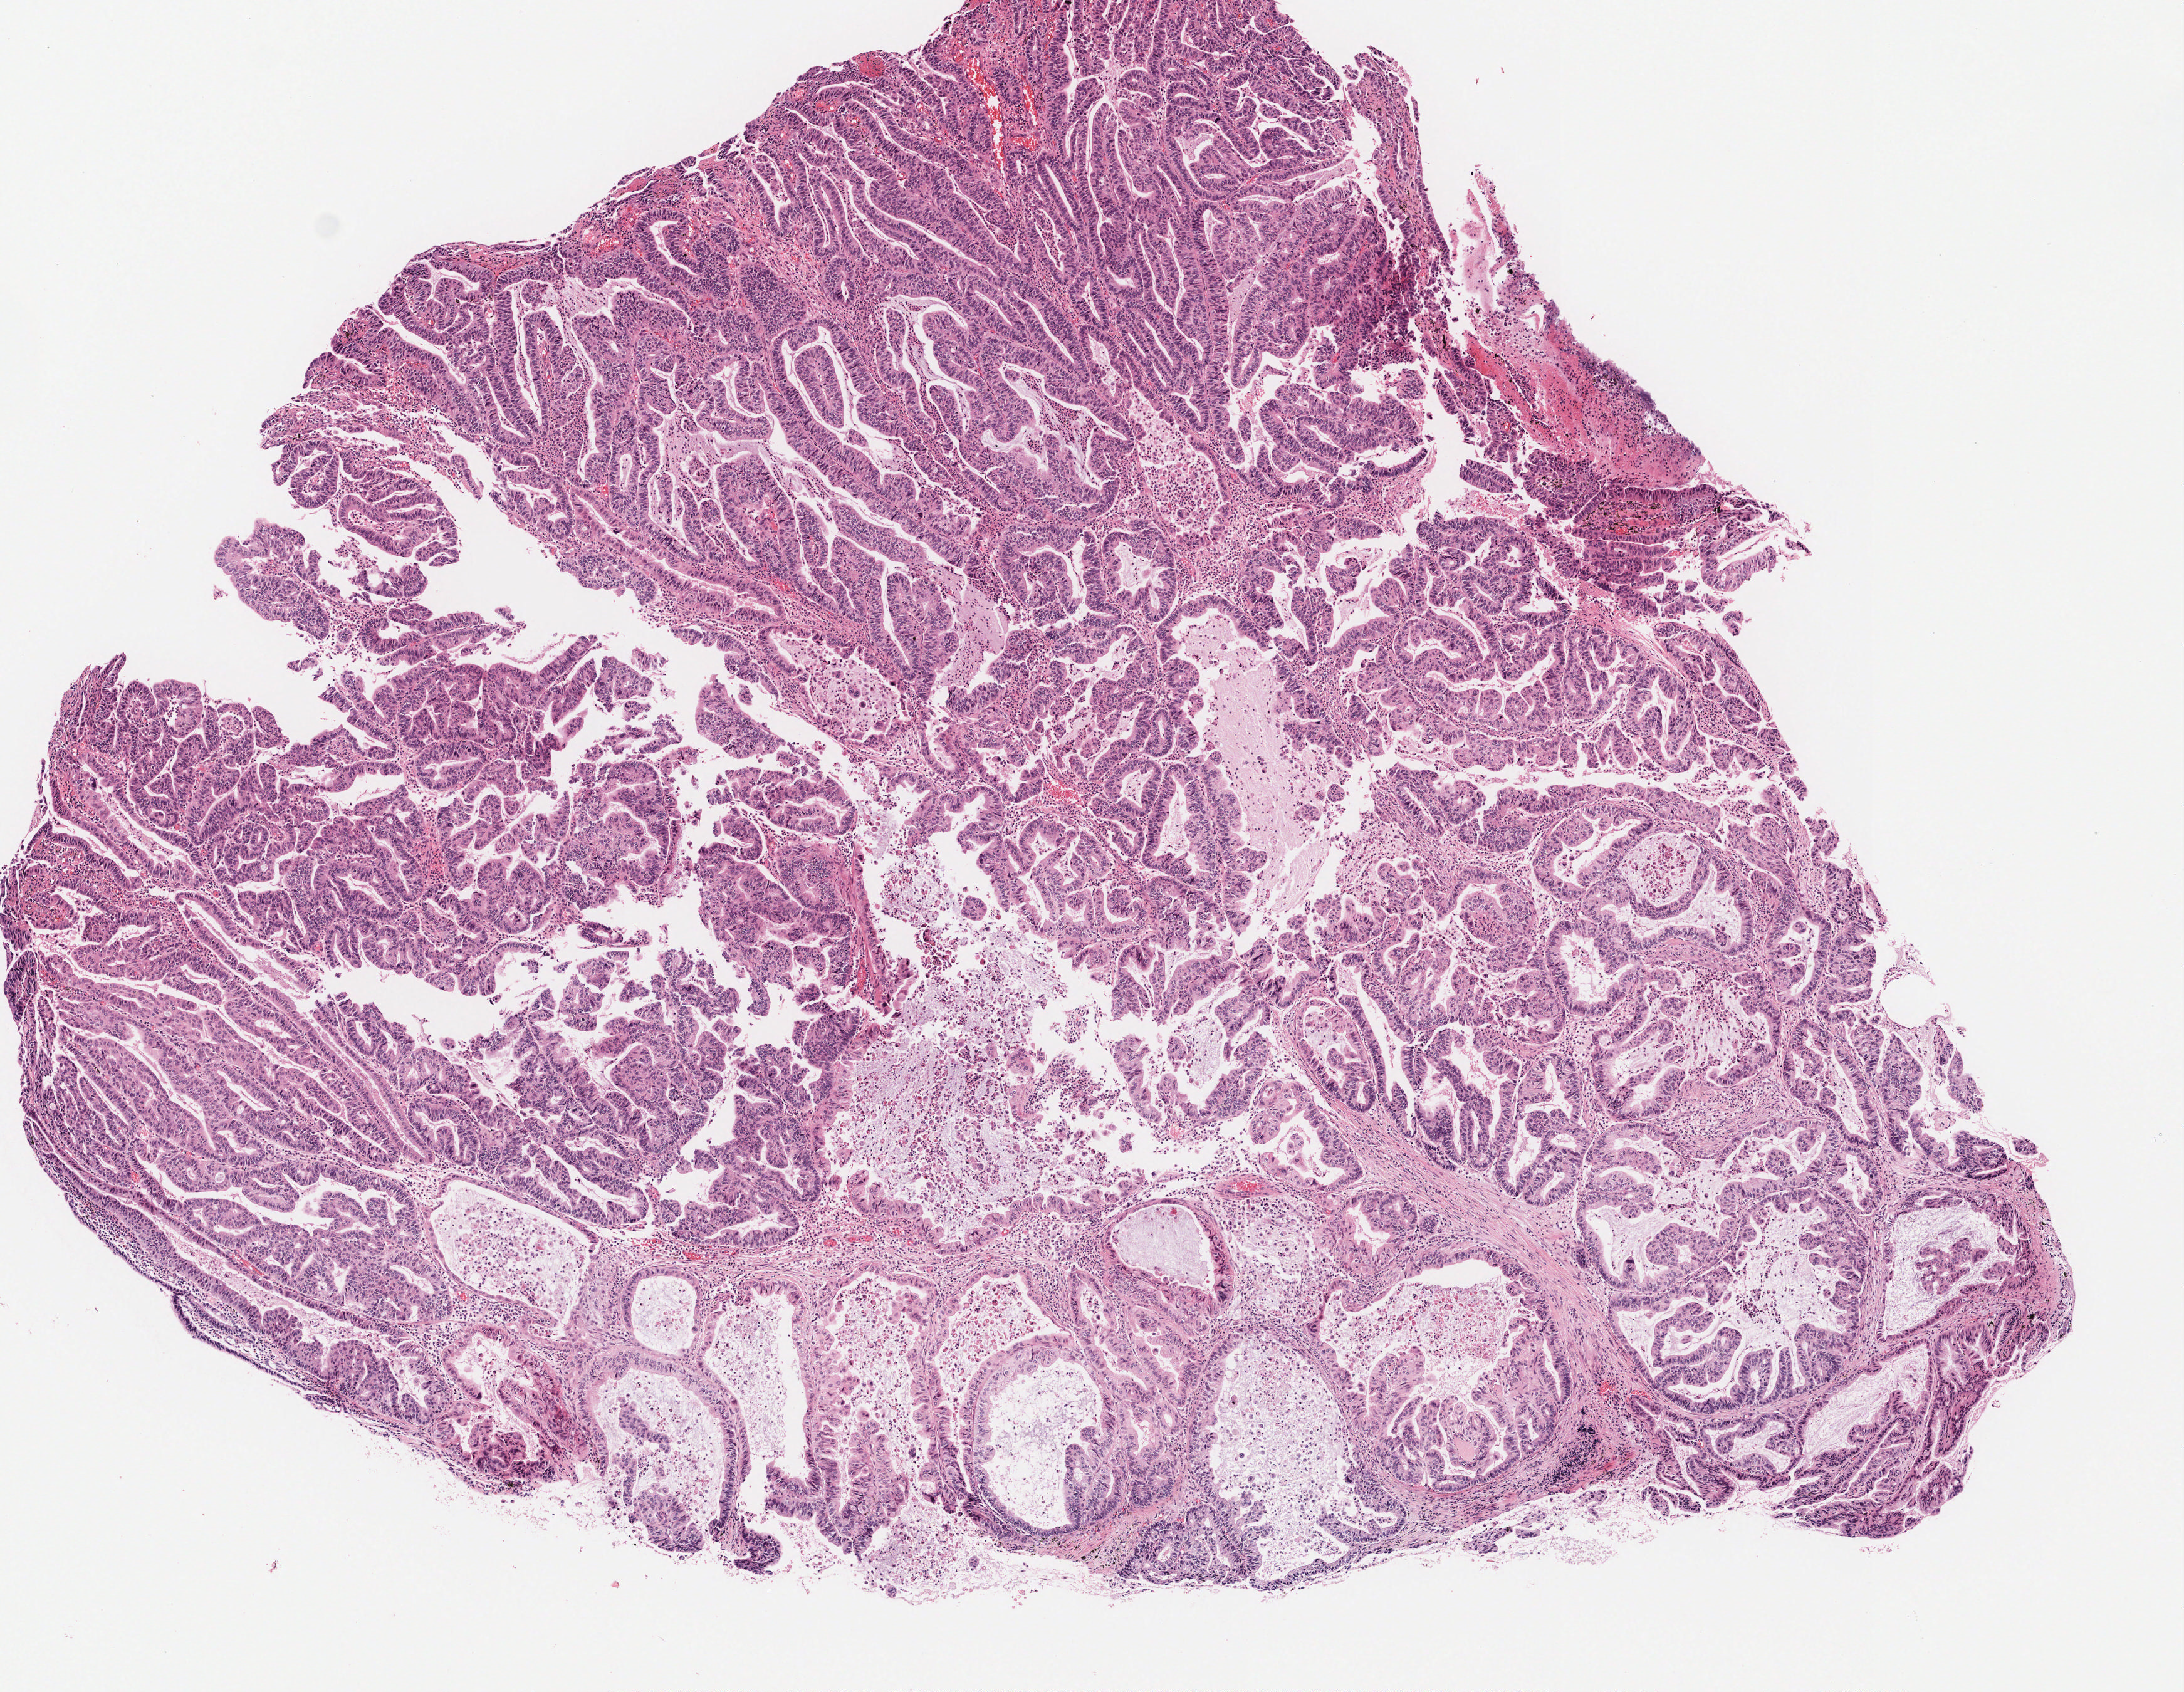
Whole-slide histology image, Hematoxylin and eosin (H&E) stained, low-resolution overview of the scanned area, about 6.9 x 5.3 mm (slide scanned at 20x). FFPE section. Primary tumour sample from the stomach. Male, age 75 years at initial diagnosis.
Diagnosis: Tubular adenocarcinoma (body of stomach).